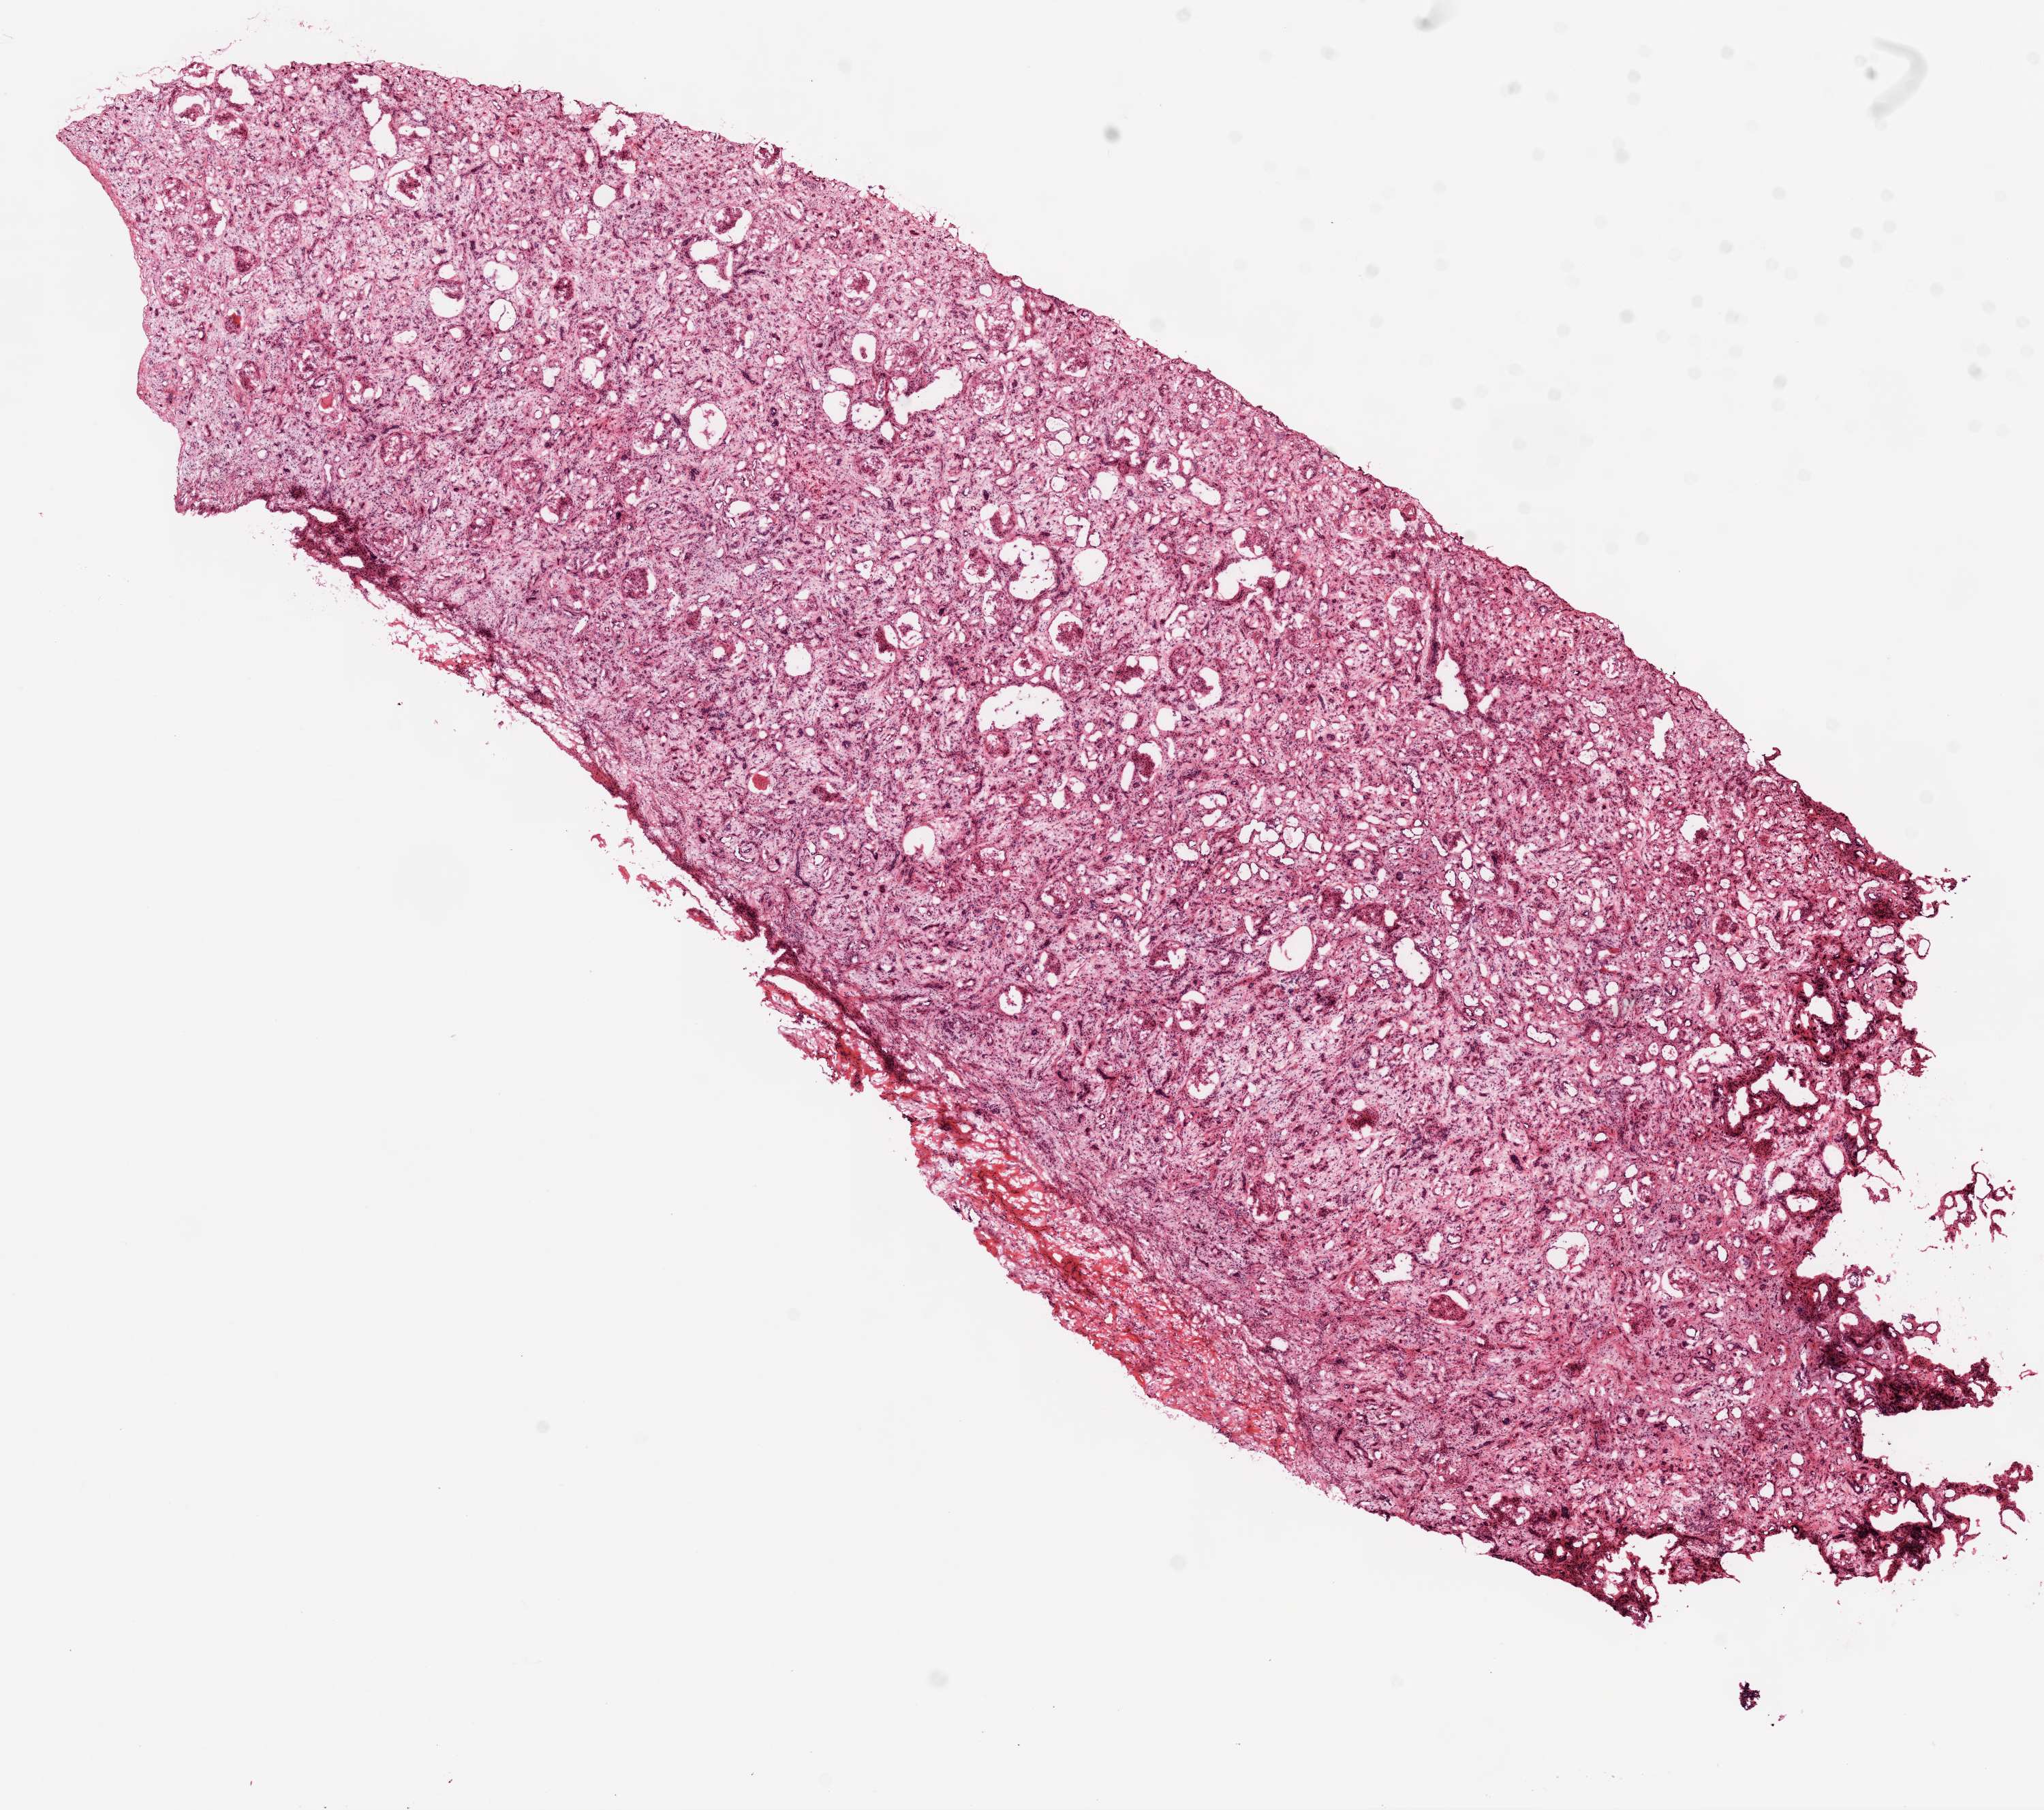
Whole-slide histology image, Hematoxylin and eosin (H&E) stained, whole scanned area (about 12.0 x 10.7 mm, acquisition: 20x scan) shown as a low-resolution overview; frozen section; sample: solid tissue normal (non-tumour tissue), kidney. Male, age 60 years at initial diagnosis.
This section: solid tissue normal (non-tumour) sample from the same patient. Patient diagnosis: Clear cell adenocarcinoma, NOS.